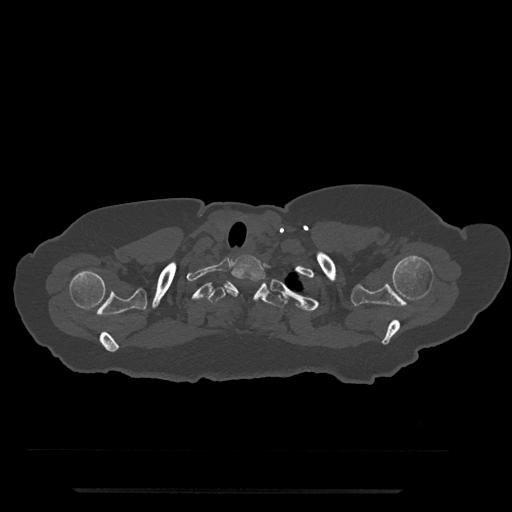
CT including the spine, one axial slice. Position 691 of 797 along the scan axis. Reconstruction kernel Br40s/3. 120 kVp. Bone window (W 1800 / L 400 HU). 512 × 512 image matrix. Patient: female, 51 years. From the clinical record (not read from this slice): primary cancer: neuro.
Structures marked on this image (semi-automatically segmented with operator editing):
- T1 vertebra: bounding box <230,254,266,297> (left, top, right, bottom; pixels)
- T2 vertebra: <207,281,286,308>